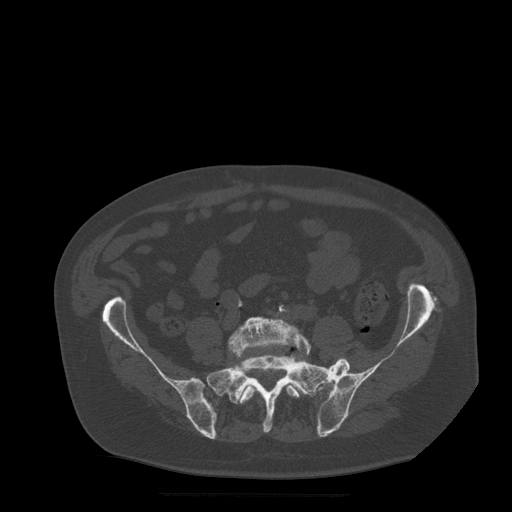
CT including the spine, one axial slice. Slice 75 of 522 in the series (ordered by position). Bone window (W 1800 / L 400 HU). 512 × 512 image matrix, field of view 420 × 420 mm. Patient age 72 years. From the clinical record (not read from this slice): primary cancer: prostate.
Outlined on this slice (semi-automatically segmented with operator editing):
- L5 vertebra: bounding box (x1, y1, x2, y2) in pixels: (228, 317, 312, 404)